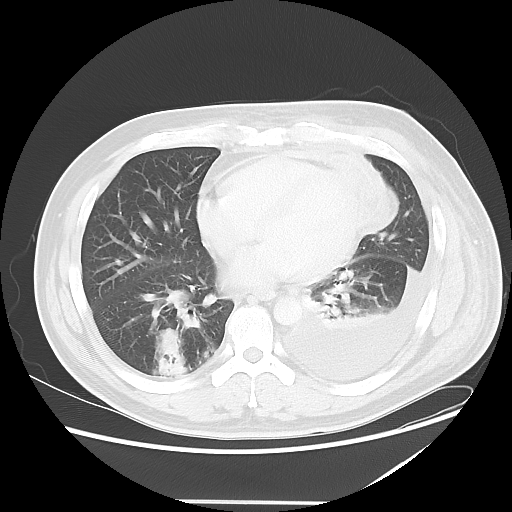
Chest CT, one axial slice. Slice 19 of 52 in the series (ordered by position). Reconstruction kernel LUNG. 120 kVp. Lung window (W 1500 / L -600 HU). 5 mm slice thickness. 512 × 512 image matrix, field of view 405 × 405 mm. Male patient, age 42 years. Case-level facts recorded for this patient, not image findings: clinical TNM (as recorded): T2 N1 M1.
Structures marked on this image (bounding box drawn by a radiologist):
- lung tumour (recorded histology: adenocarcinoma): bounding box [x1, y1, x2, y2] px = [151, 325, 181, 362]